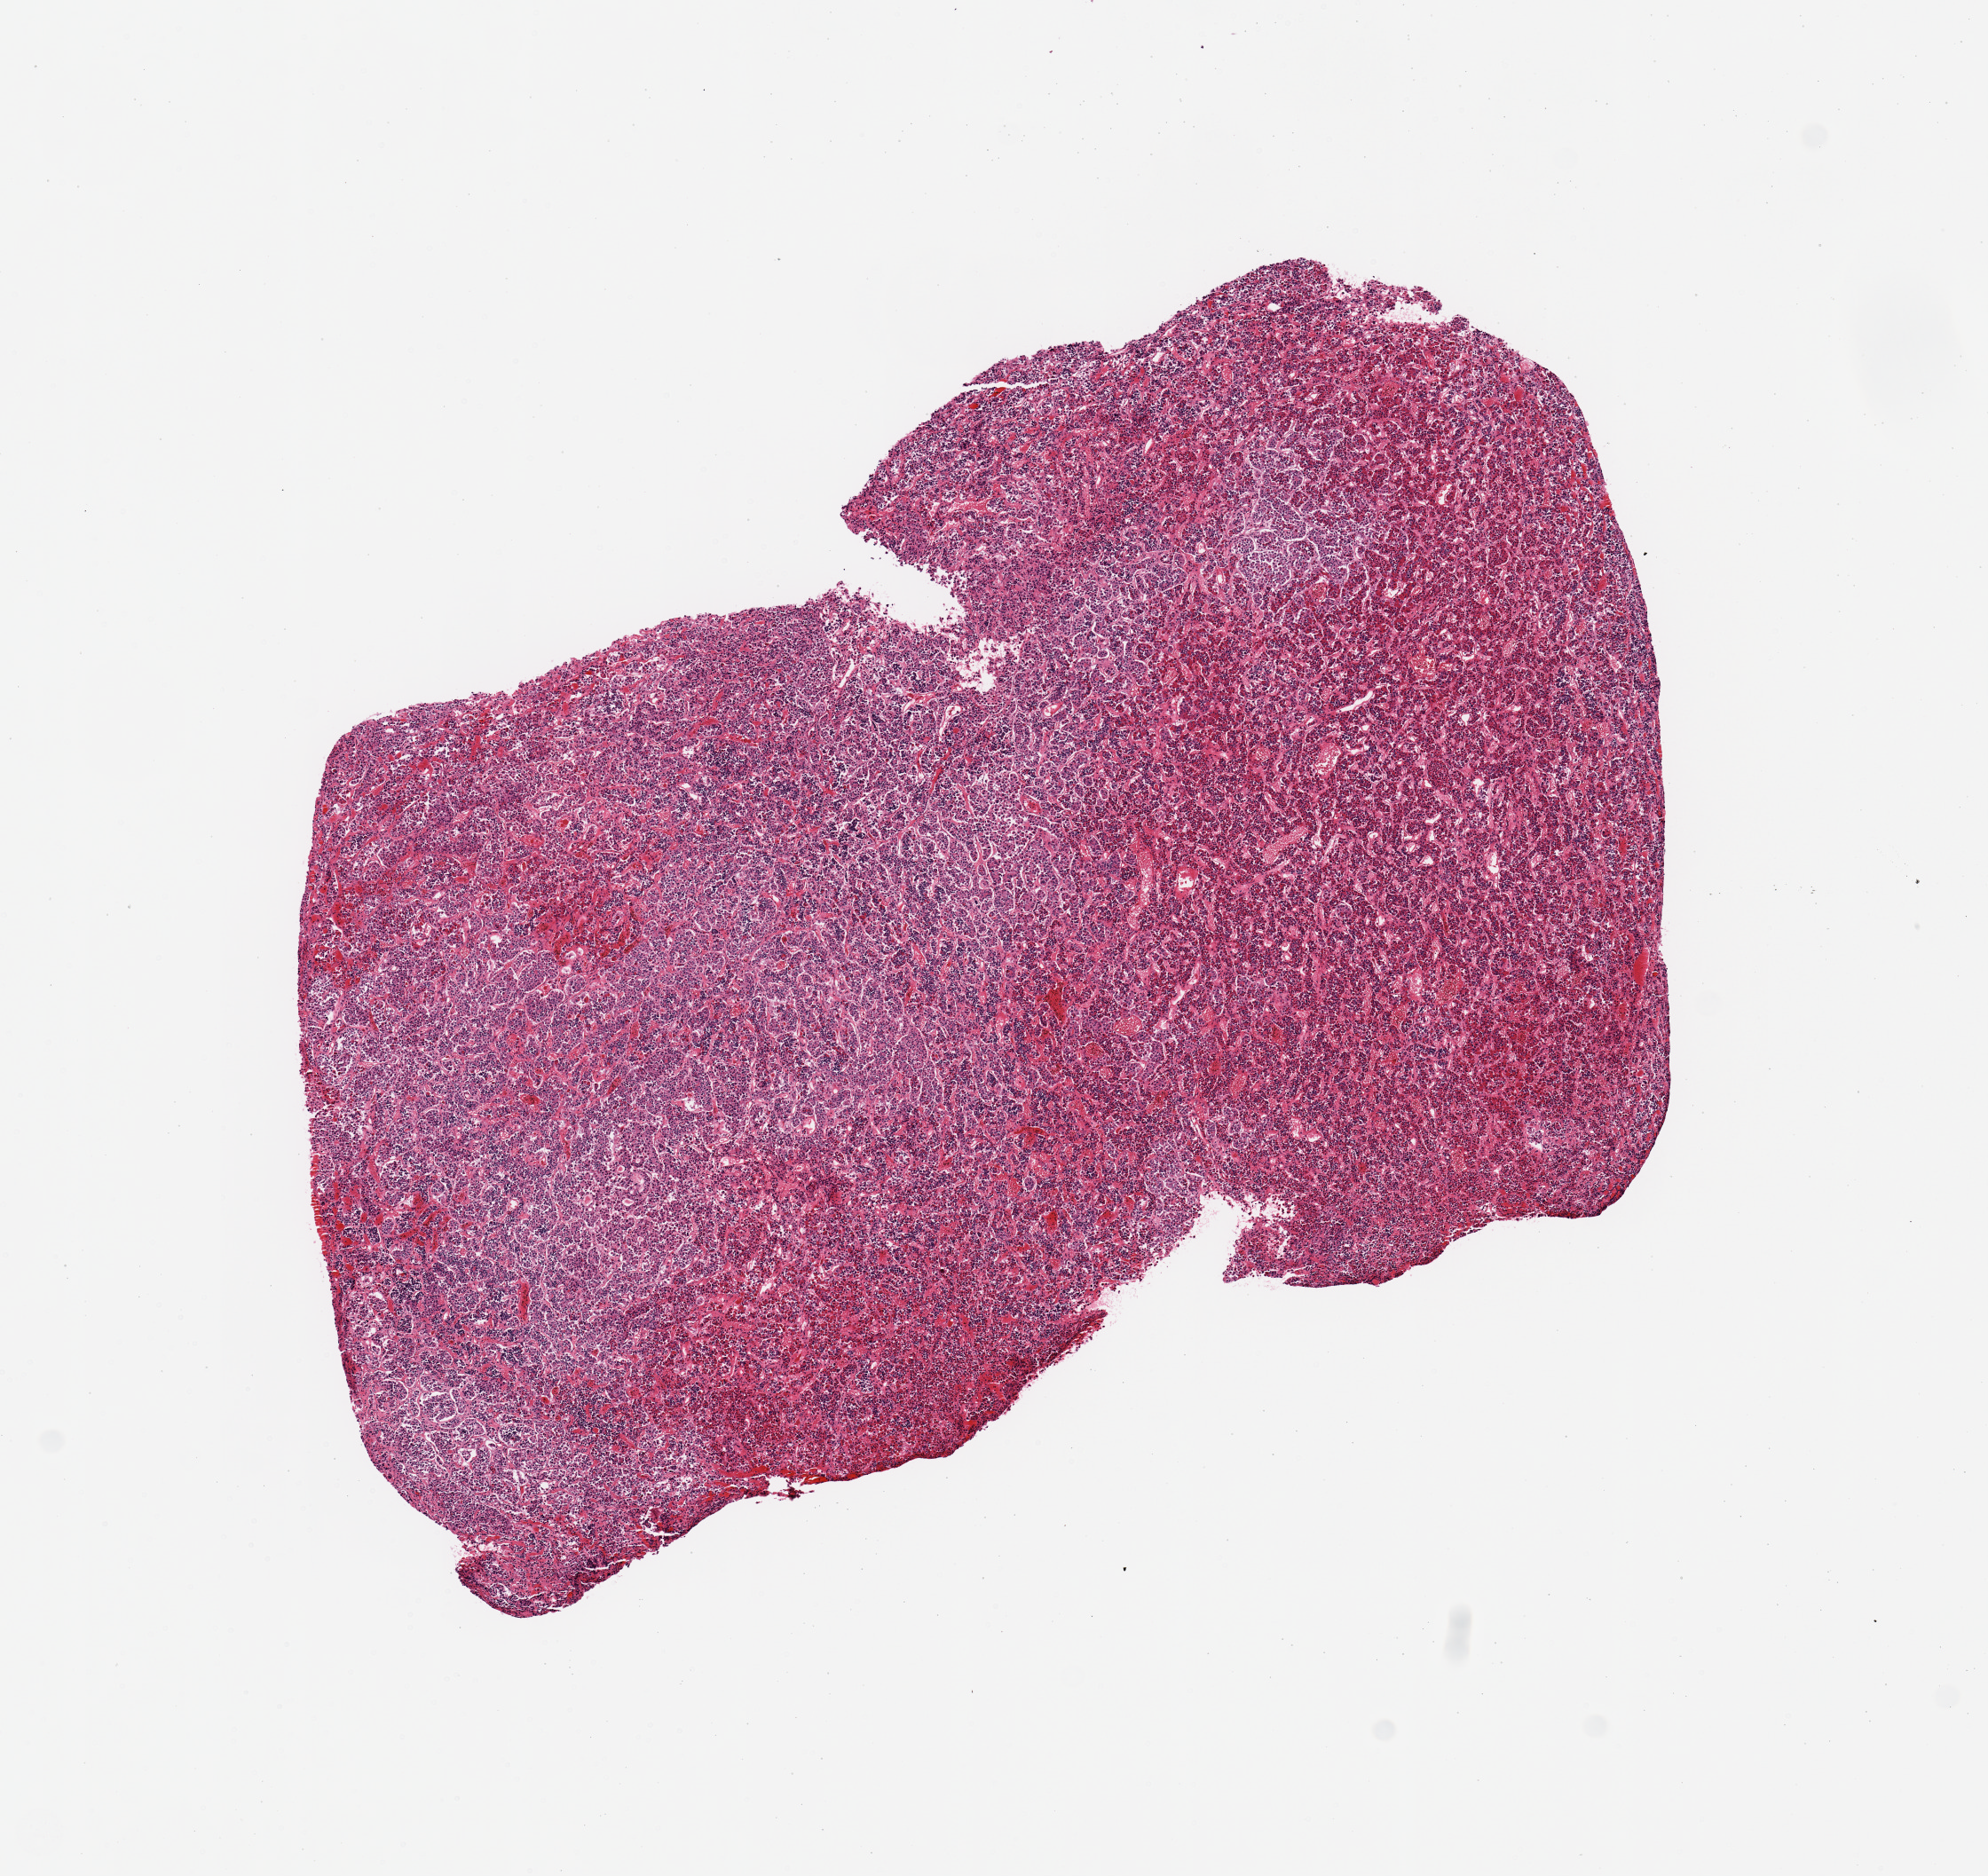
Digitized H&E-stained section, brightfield — whole scanned area (about 8.9 x 8.4 mm) shown as a low-resolution overview, PAXgene-fixed, paraffin-embedded tissue, sampled site (target tissue): pituitary, donor tissue sample. Female donor.
- review note (as recorded): 1 piece, all adenohypophysis; no abnormalities